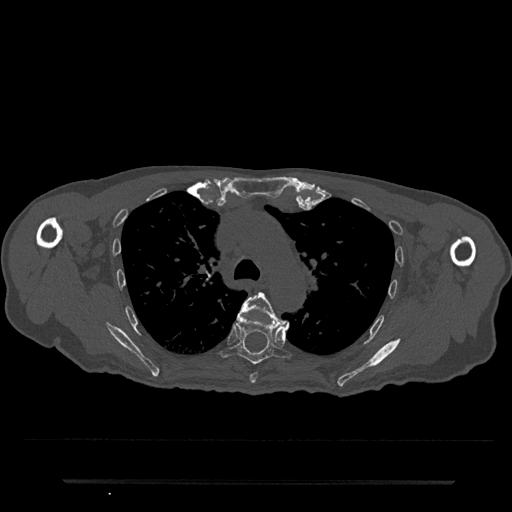
CT including the spine, one axial slice; position 544 of 797 along the scan axis; reconstruction kernel Br40s/3; bone window (W 1800 / L 400 HU); 0.5 mm slice thickness; 512 × 512 image matrix, field of view 427 × 427 mm. Patient: male, 74 years. From the clinical record (not read from this slice): primary cancer: prostate.
Annotated regions visible in this slice (semi-automatic segmentation, software-assisted and operator-edited):
- T5 vertebra: box from (x=239, y=292) to (x=289, y=384) px
- T6 vertebra: (x=217, y=314)–(x=293, y=365)